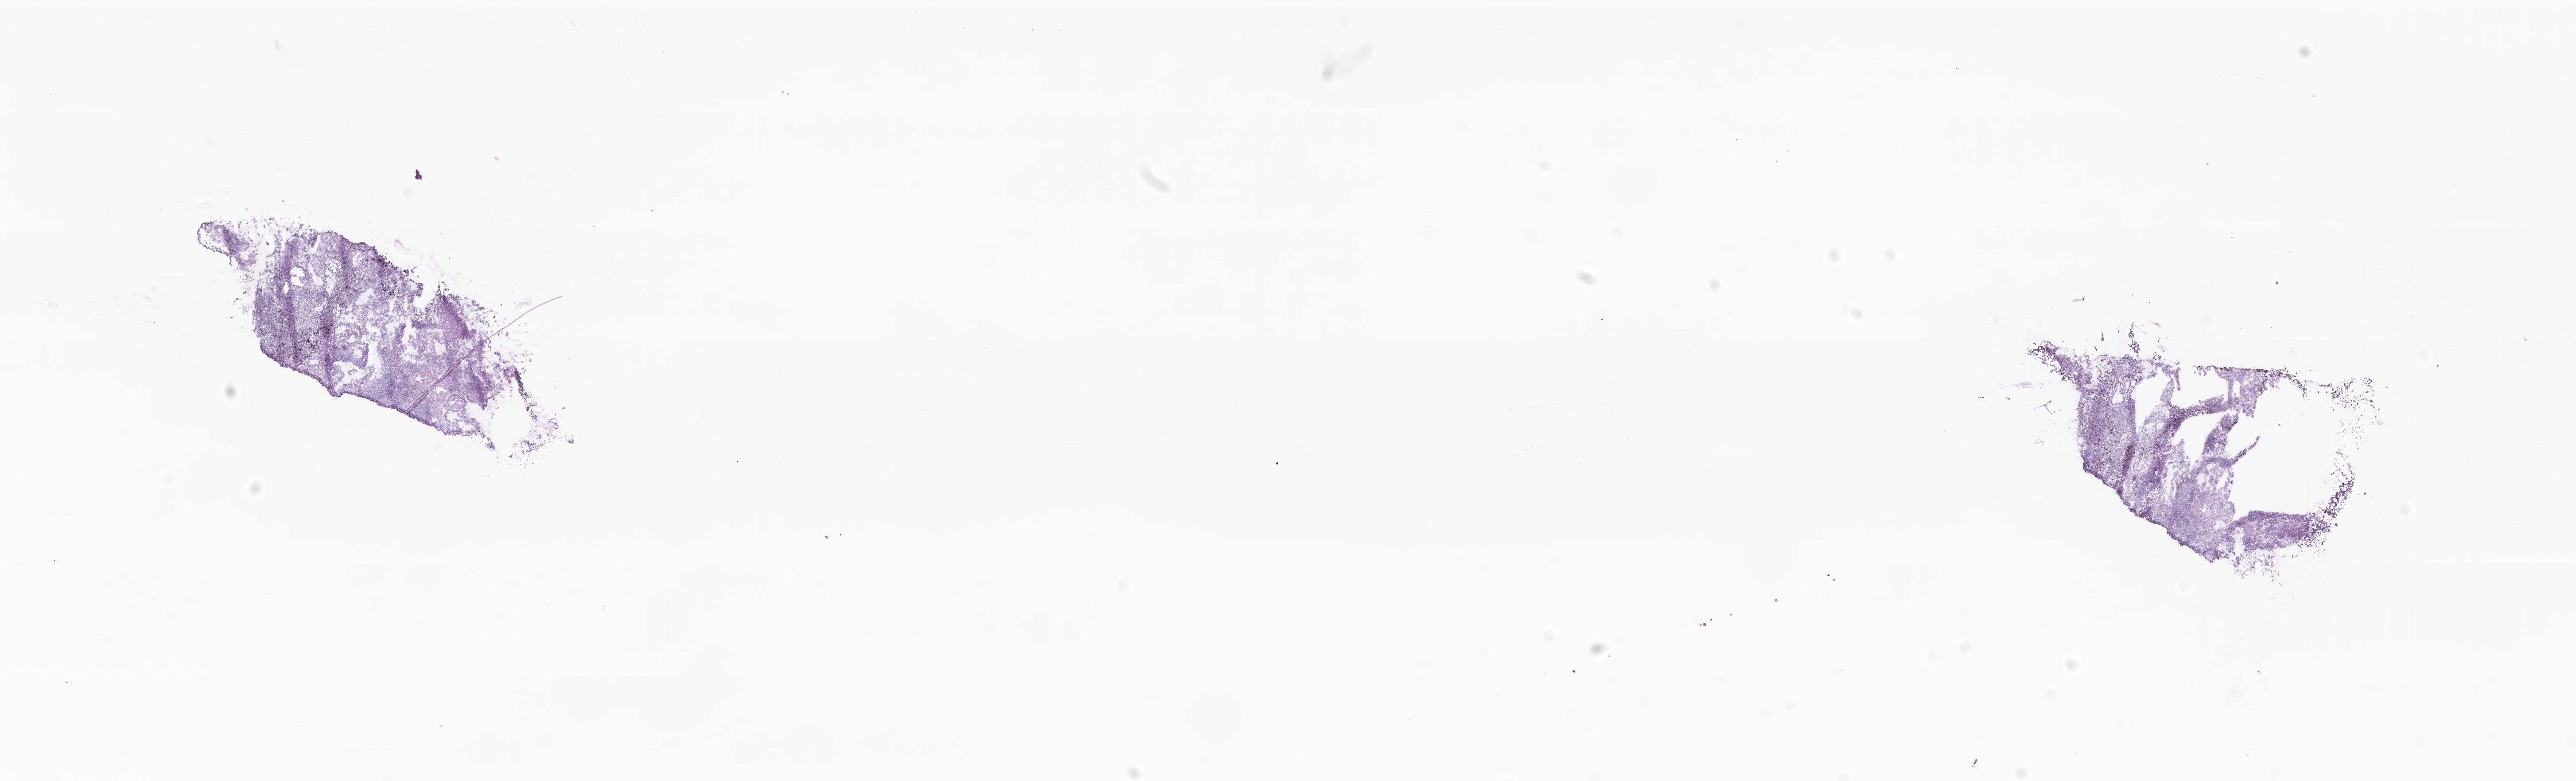
Haematoxylin and eosin whole-slide image — a low-resolution overview of the entire scanned area, about 24.5 x 7.4 mm. Frozen section (tissue freezing medium). Metastatic tumor tissue. Patient: male, age at initial diagnosis 72 years. Slide review estimates, as recorded: tumor cells 26%, tumor nuclei 35%, stromal cells 74%, necrosis 0%, normal cells 0%. Inflammatory infiltration, as recorded: lymphocyte infiltration 60%, monocyte infiltration 2%, neutrophil infiltration 0%.
* patient diagnosis (primary): Mucinous adenocarcinoma